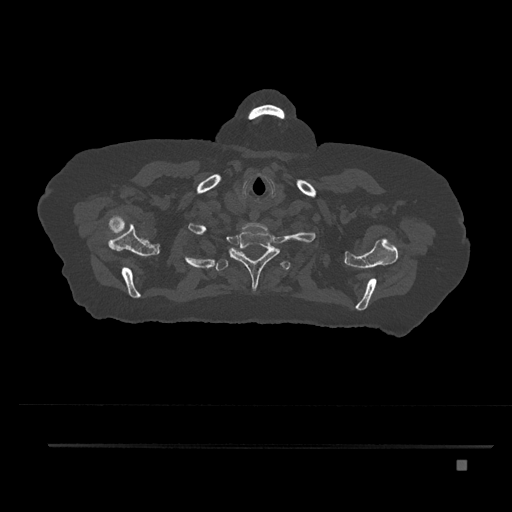
CT including the spine, one axial slice; position 694 of 797 along the scan axis; 120 kVp; bone window (W 1800 / L 400 HU); 0.5 mm slice thickness; 512 × 512 image matrix, field of view 437 × 437 mm. Patient: female, 76 years. Case-level facts recorded for this patient, not image findings: primary cancer: lung; vertebrae with lytic lesions (as recorded): T11, L3.
Outlined on this slice (semi-automatic segmentation, software-assisted and operator-edited):
- T1 vertebra: bounding box (x1, y1, x2, y2) in pixels: (229, 228, 280, 291)
- T2 vertebra: (207, 248, 290, 271)